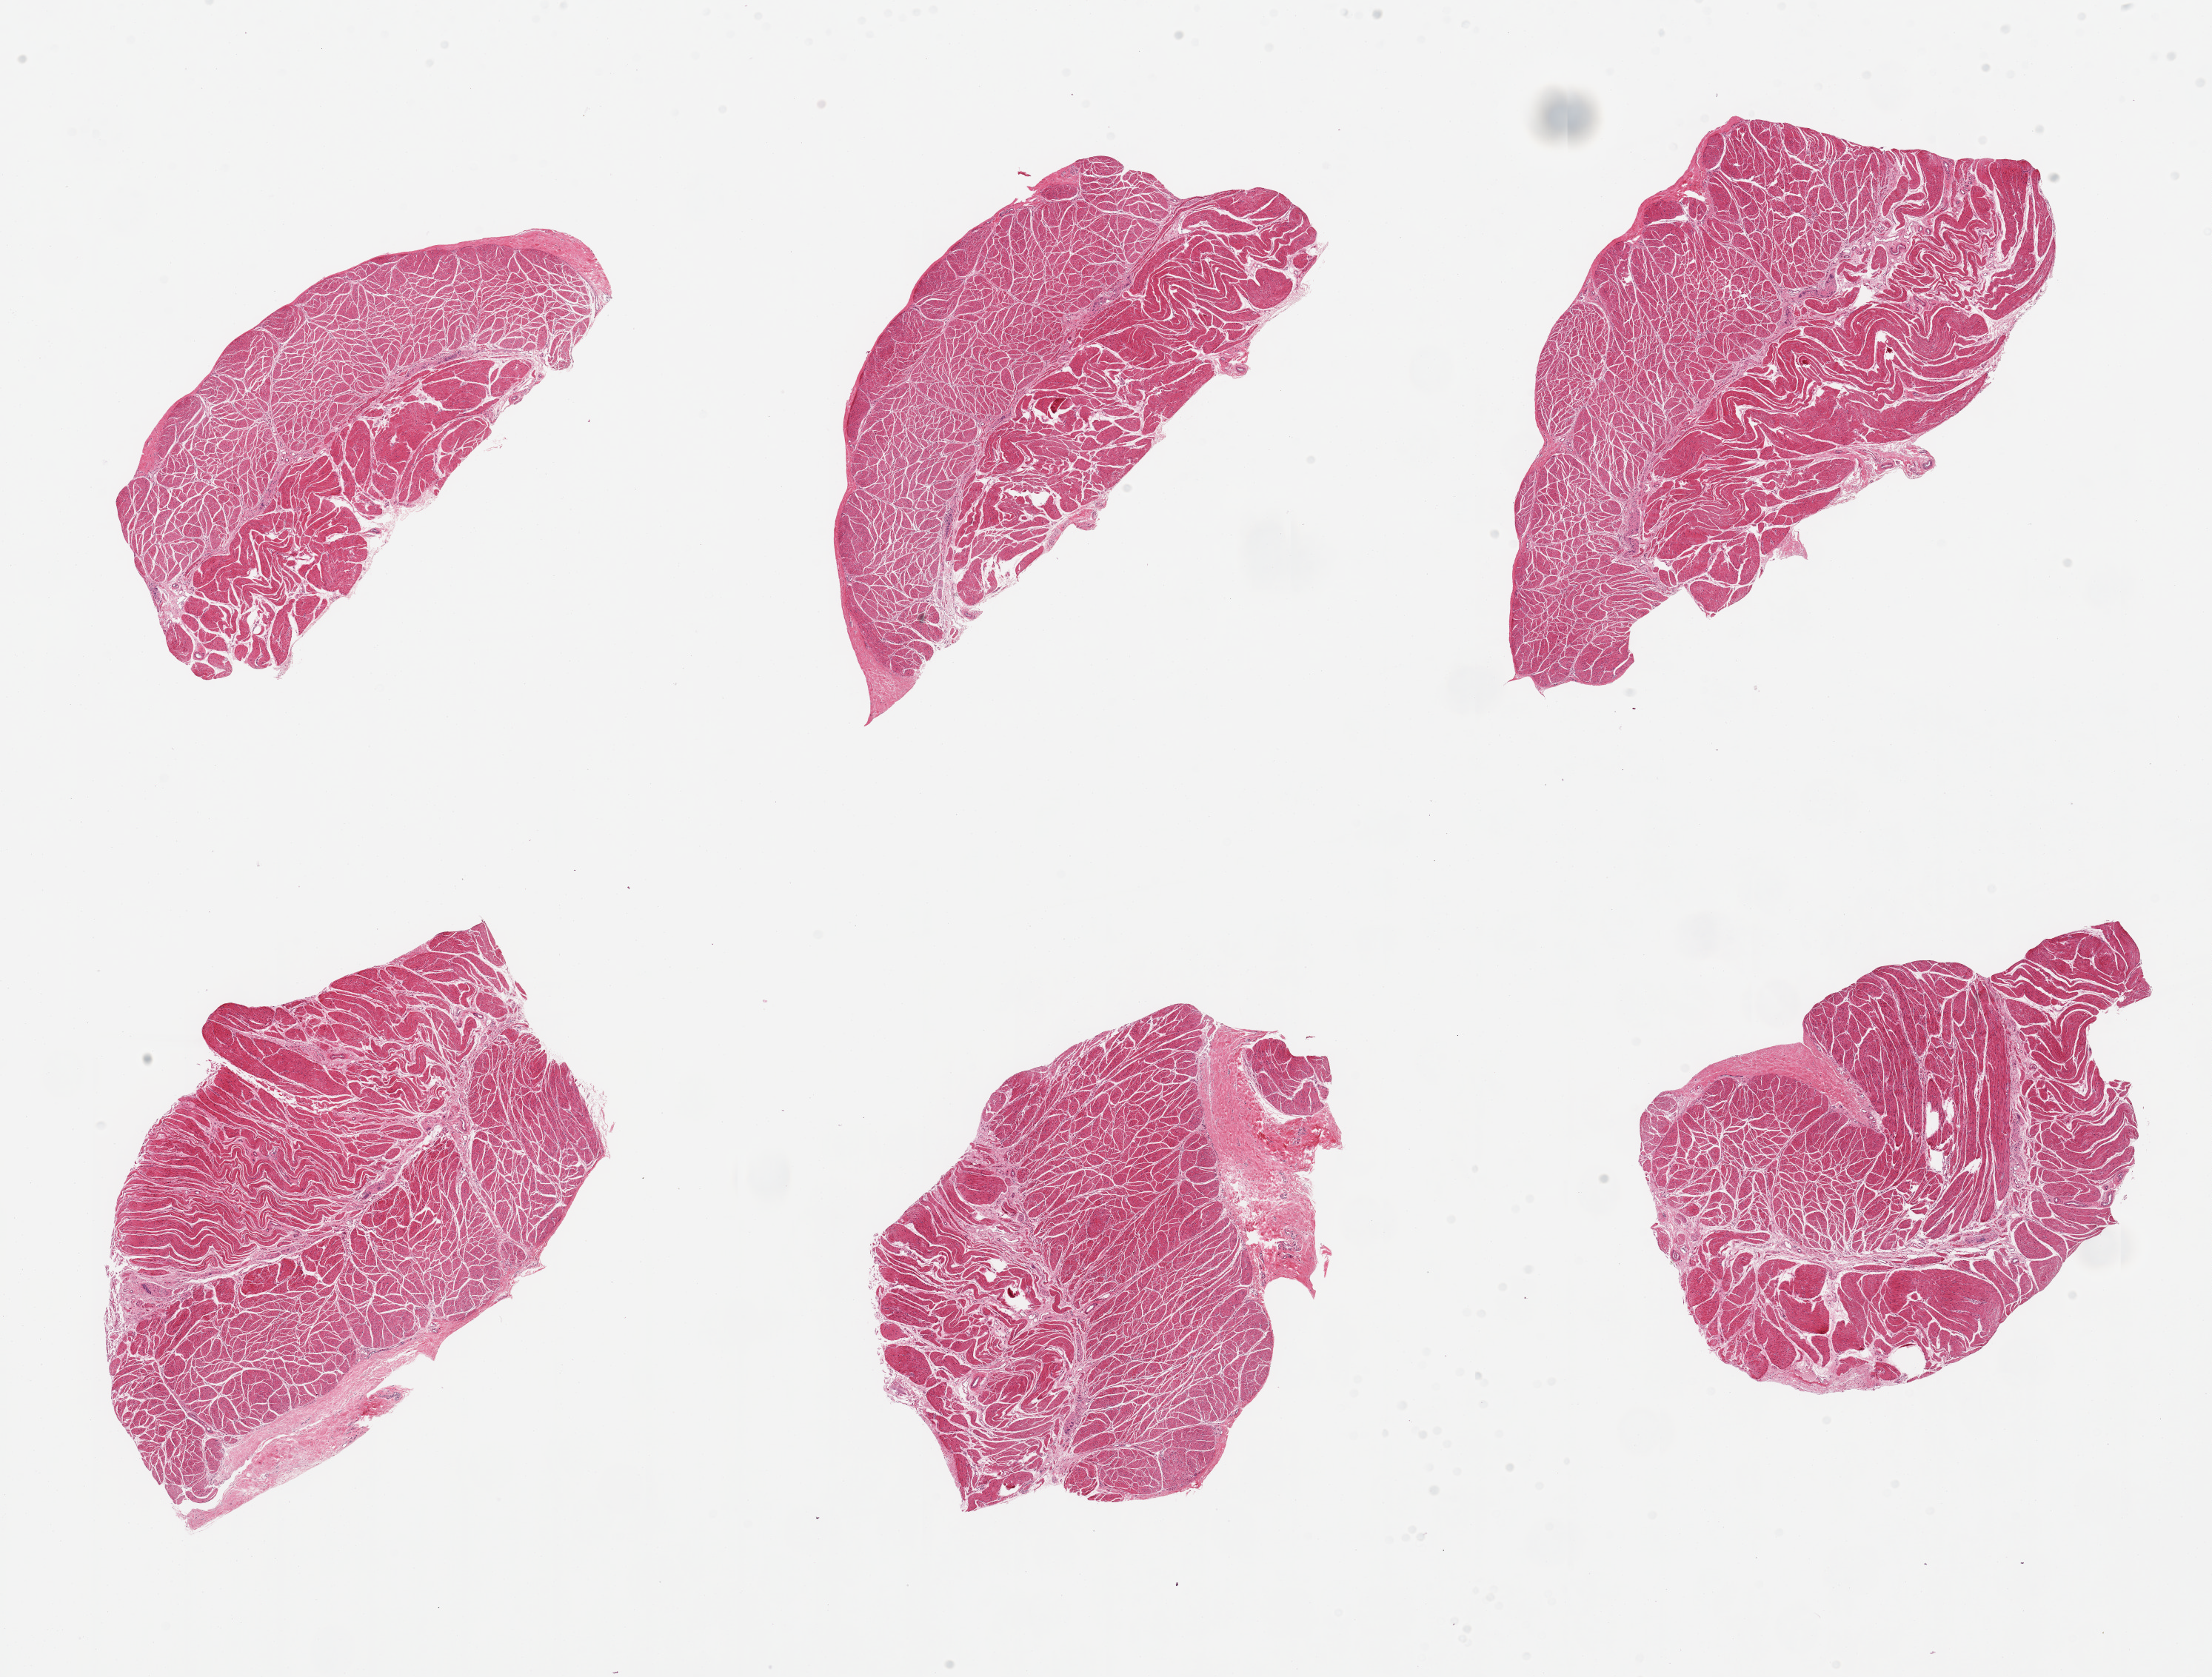
Digitized H&E-stained section, brightfield, shown as a low-resolution overview of the whole scanned area (about 23.6 x 17.9 mm). PAXgene-fixed, paraffin-embedded tissue. Section of esophageal muscle (target tissue). Tissue donor sample. Donor: female.
• reviewer comment on this tissue sample: 6 pieces; well trimmed